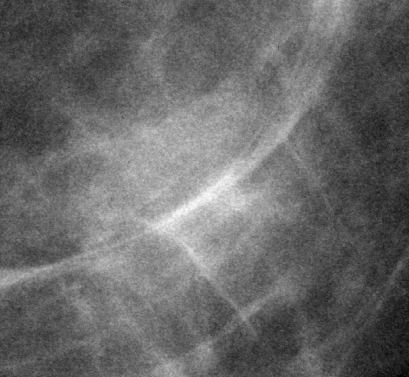
Region of interest cut from a scanned film mammogram (one marked finding); left breast; CC view; BI-RADS breast density category 1 (scale 1–4).
- Marked abnormality: calcifications, morphology pleomorphic, distribution clustered; BI-RADS assessment category 3; subtlety rating 3 on a 1 (subtle) to 5 (obvious) scale; pathology (as recorded): benign.